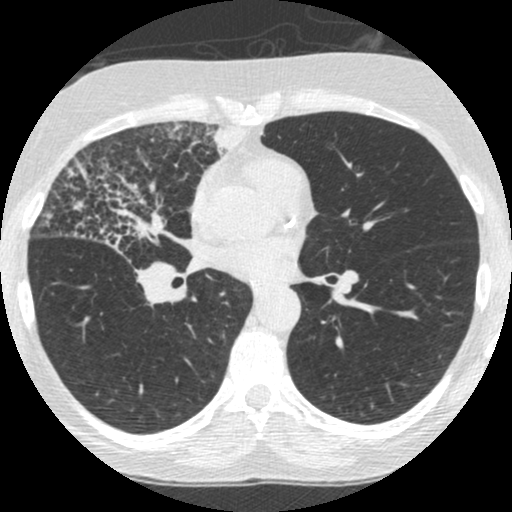
Low-dose screening chest CT, one axial slice. Position 134 of 253 along the scan axis. 120 kVp. Lung window (W 1500 / L -600 HU). 1.25 mm slice thickness. 512 × 512 image matrix, field of view 294 × 294 mm.
Outlined on this slice (outlined manually by an expert reader):
- lesion 2 (tumor, hilum of right lung): bounding box <42,148,195,259> (left, top, right, bottom; pixels)
- lesion 4 (tumor, upper lobe of right lung): <206,124,252,161>